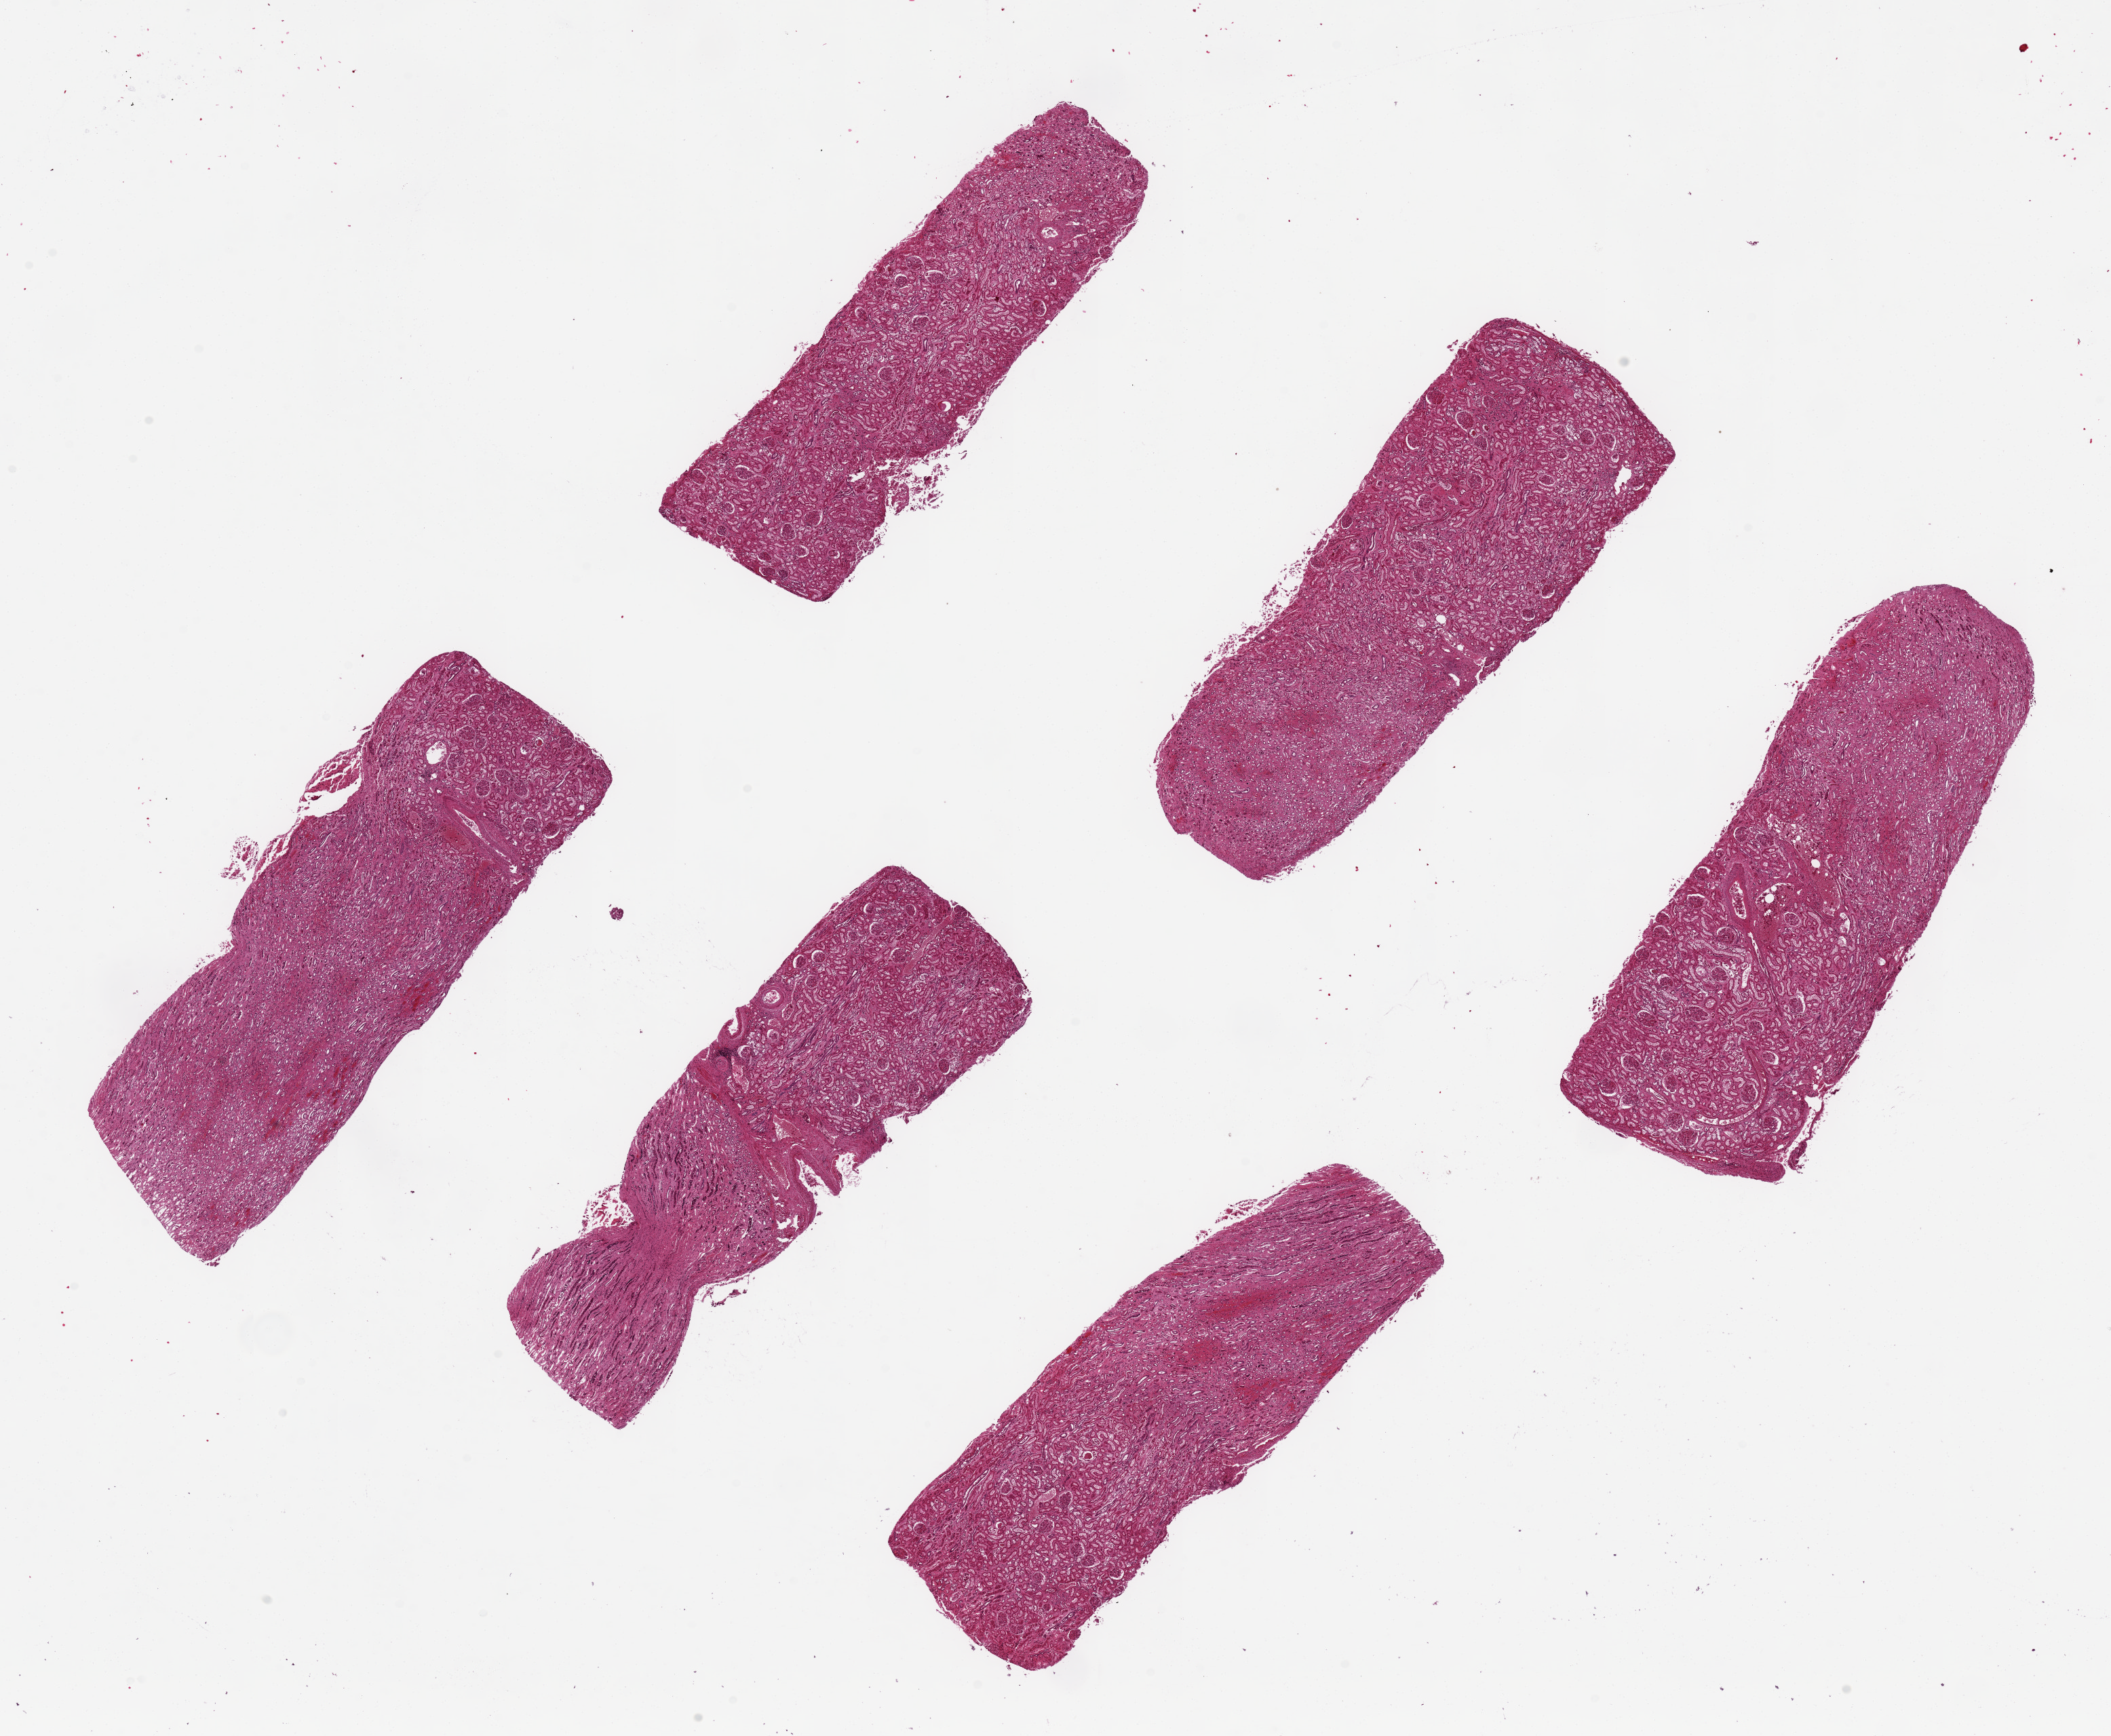
Digitized H&E-stained section, brightfield — whole scanned area (about 24.6 x 20.2 mm) shown as a low-resolution overview, PAXgene-fixed, paraffin-embedded tissue, section of renal cortex (target tissue), tissue donor sample. Donor sex: female.
Review note (as recorded): 6 pieces, ~7x2.5mm. Minor components of 'contaminating' medulla, noted on images.